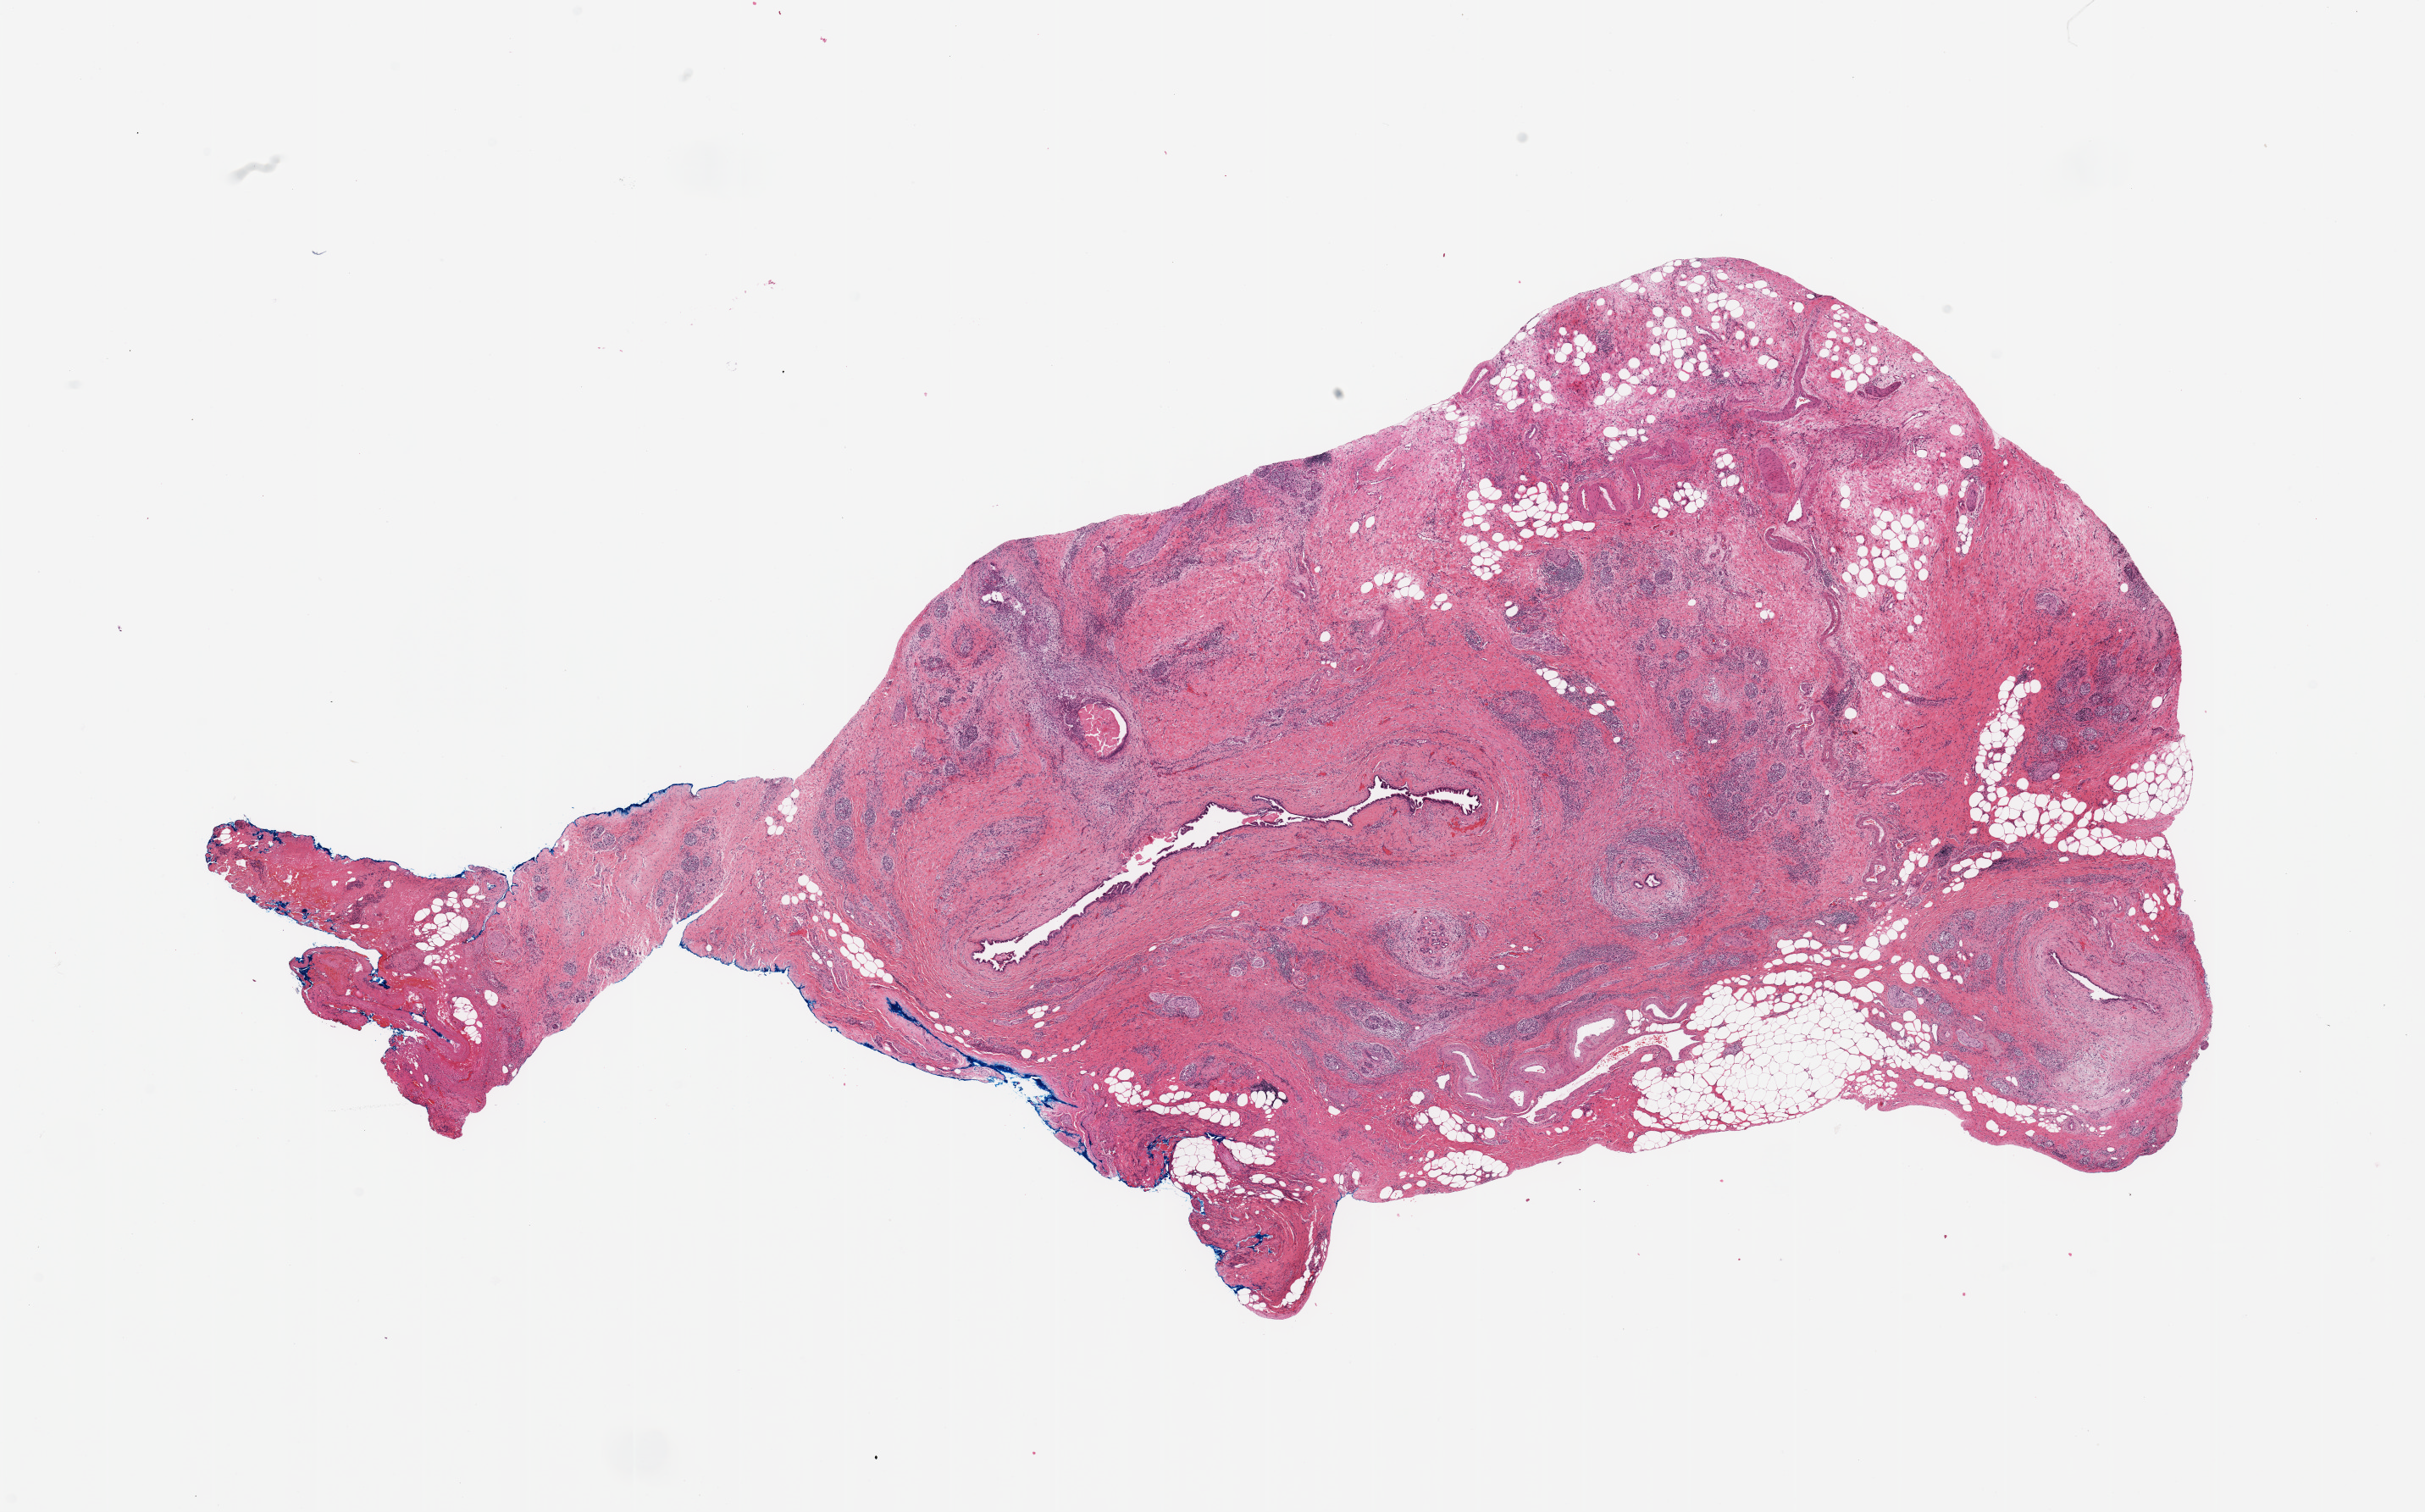
Digitized Hematoxylin and eosin (H&E) stained tissue section (whole slide) — shown as a low-resolution overview of the whole scanned area (about 22.6 x 14.1 mm, acquisition: 20x scan), pancreas, tumour tissue. Female, 64 y/o.
Histologic diagnosis: Infiltrating duct carcinoma, NOS.